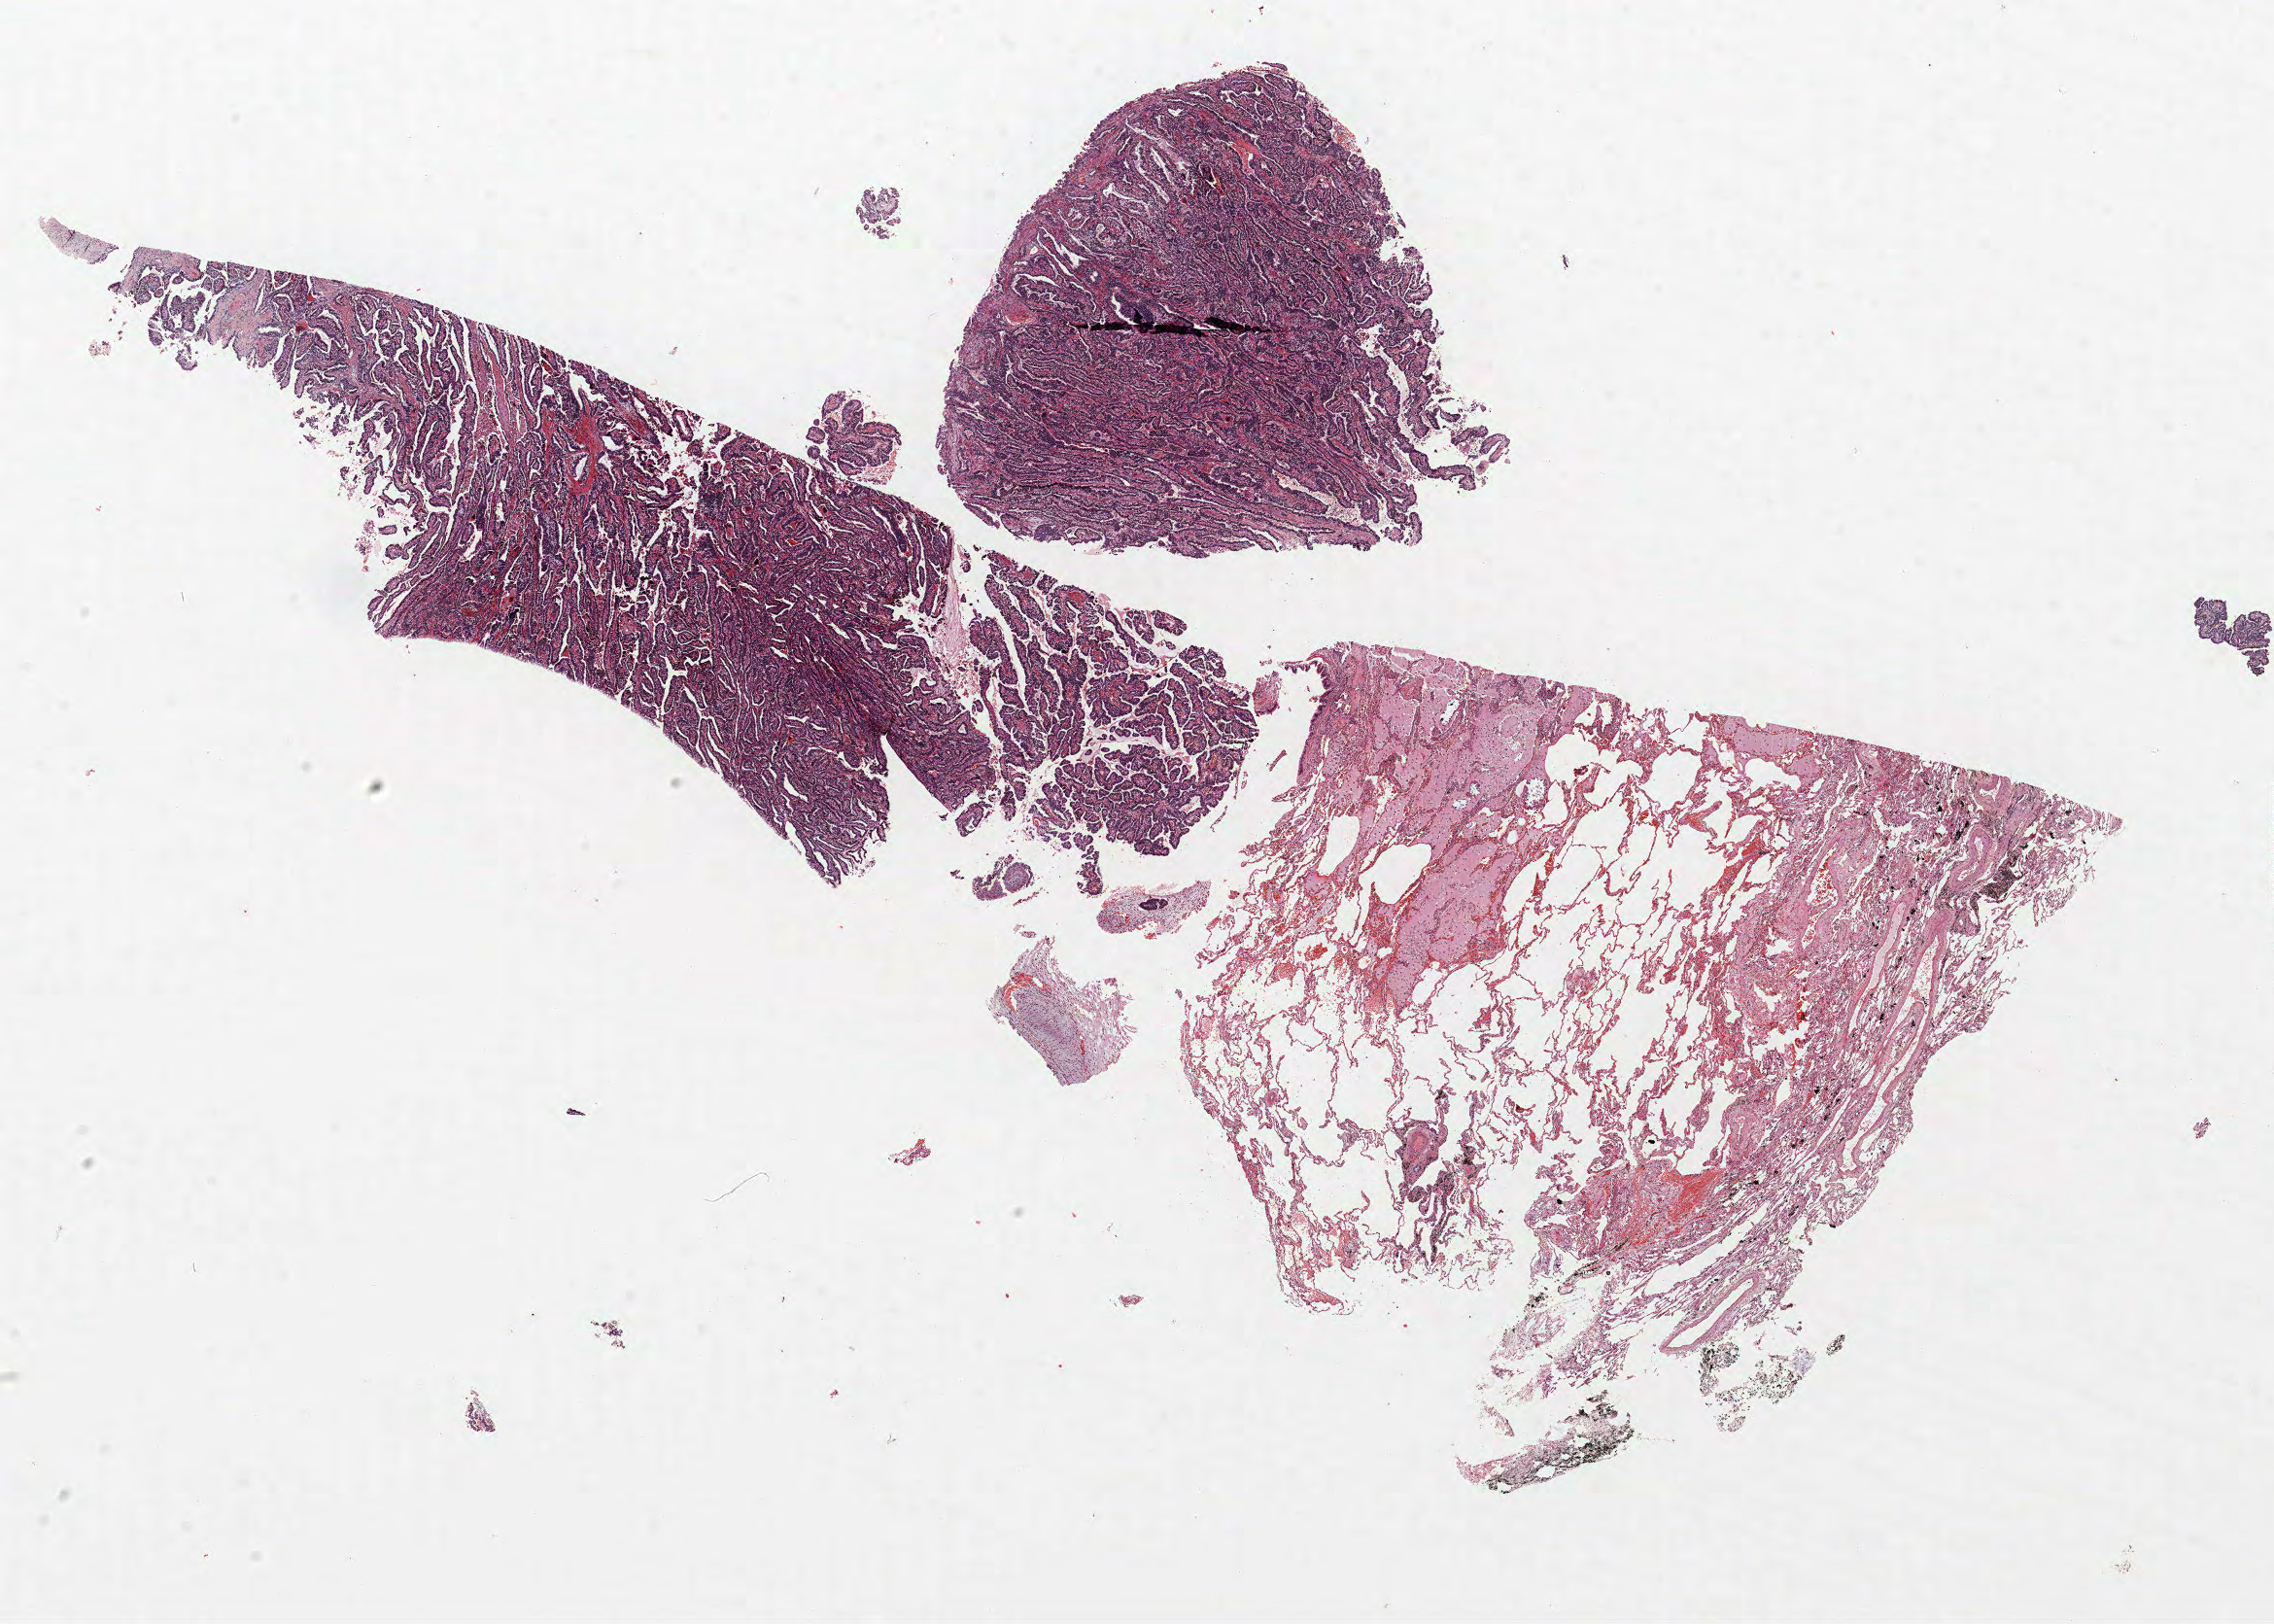
Hematoxylin and eosin (H&E) stained whole-slide image — low-resolution overview of the scanned area, about 18.7 x 13.4 mm (acquisition: 40x scan). FFPE section. Lung tissue. Male, age 58 at enrolment. Grade: well differentiated (G1).
- tumour size (pathology): 17 mm
- primary tumour location (clinical record): left upper lobe
- participant's lung-cancer diagnosis: Bronchiolo-alveolar adenocarcinoma, NOS (ICD-O-3 8250/3)
- stage (AJCC 6th edition): IA